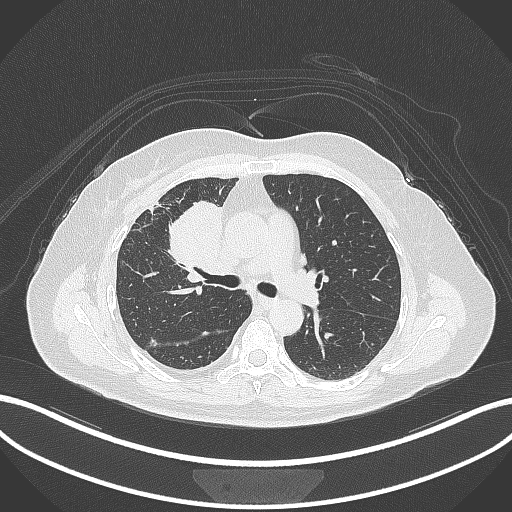
Chest CT, one axial slice. Position 173 of 305 along the scan axis. Reconstruction kernel B70f. 120 kVp. Lung window (W 1500 / L -600 HU). 512 × 512 image matrix, field of view 400 × 400 mm. Female patient, age 52 years. Case-level facts recorded for this patient, not image findings: clinical TNM (as recorded): T3 N1 M1.
Annotated regions visible in this slice (rectangle marked by the reading radiologist):
- lung tumour (recorded histology: adenocarcinoma): bounding box (x1, y1, x2, y2) in pixels: (169, 194, 223, 280)